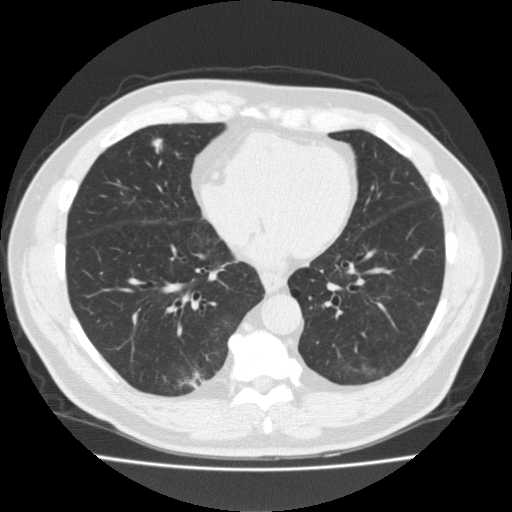
Low-dose screening chest CT, one axial slice. 120 kVp. Lung window (W 1500 / L -600 HU). 512 × 512 image matrix, field of view 369 × 369 mm.
Structures marked on this image (expert manual segmentation):
- lesion 1 (tumor, middle lobe of right lung): box from (x=153, y=138) to (x=162, y=153) px